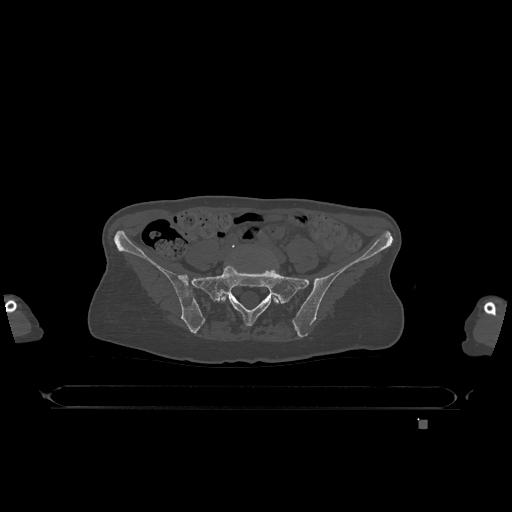
CT including the spine, one axial slice; position 201 of 1317 along the scan axis; bone window (W 1800 / L 400 HU); 0.5 mm slice thickness; 512 × 512 image matrix. Female patient, age 74 years. From the clinical record (not read from this slice): primary cancer: lung; vertebrae with lytic lesions (as recorded): T1, T4, T5, T6, L4, L5.
Annotated regions visible in this slice (semi-automatically segmented with operator editing):
- L5 vertebra: bounding box (x1, y1, x2, y2) in pixels: (220, 293, 279, 304)